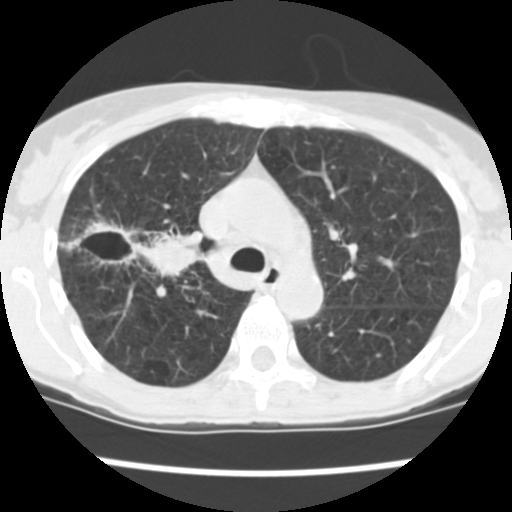
Axial slice from a low-dose chest CT screening exam. Baseline annual screen. Lung window (W 1500 / L -600 HU). 2.5 mm slice thickness. Standard (soft-tissue) reconstruction kernel (STANDARD). 512 × 512 image matrix, field of view 276 × 276 mm. Female participant, aged 60 years at enrolment. Current smoker at enrolment.
- Lesion marked by an expert reader, bounding box (x1, y1, x2, y2) in pixels: (83, 216, 194, 284).
- The screening reader recorded 3 non-calcified nodules or masses ≥4 mm on this exam; which of them this box marks is not recorded.
- Official screen result: positive, change unspecified: nodule(s) >= 4 mm or enlarging nodule(s), mass(es), or other non-specific abnormalities suspicious for lung cancer.
- Lung cancer was diagnosed 19 days after this screen: non-small cell carcinoma, right upper lobe, stage IV (AJCC 6th edition), 26 mm at pathology.